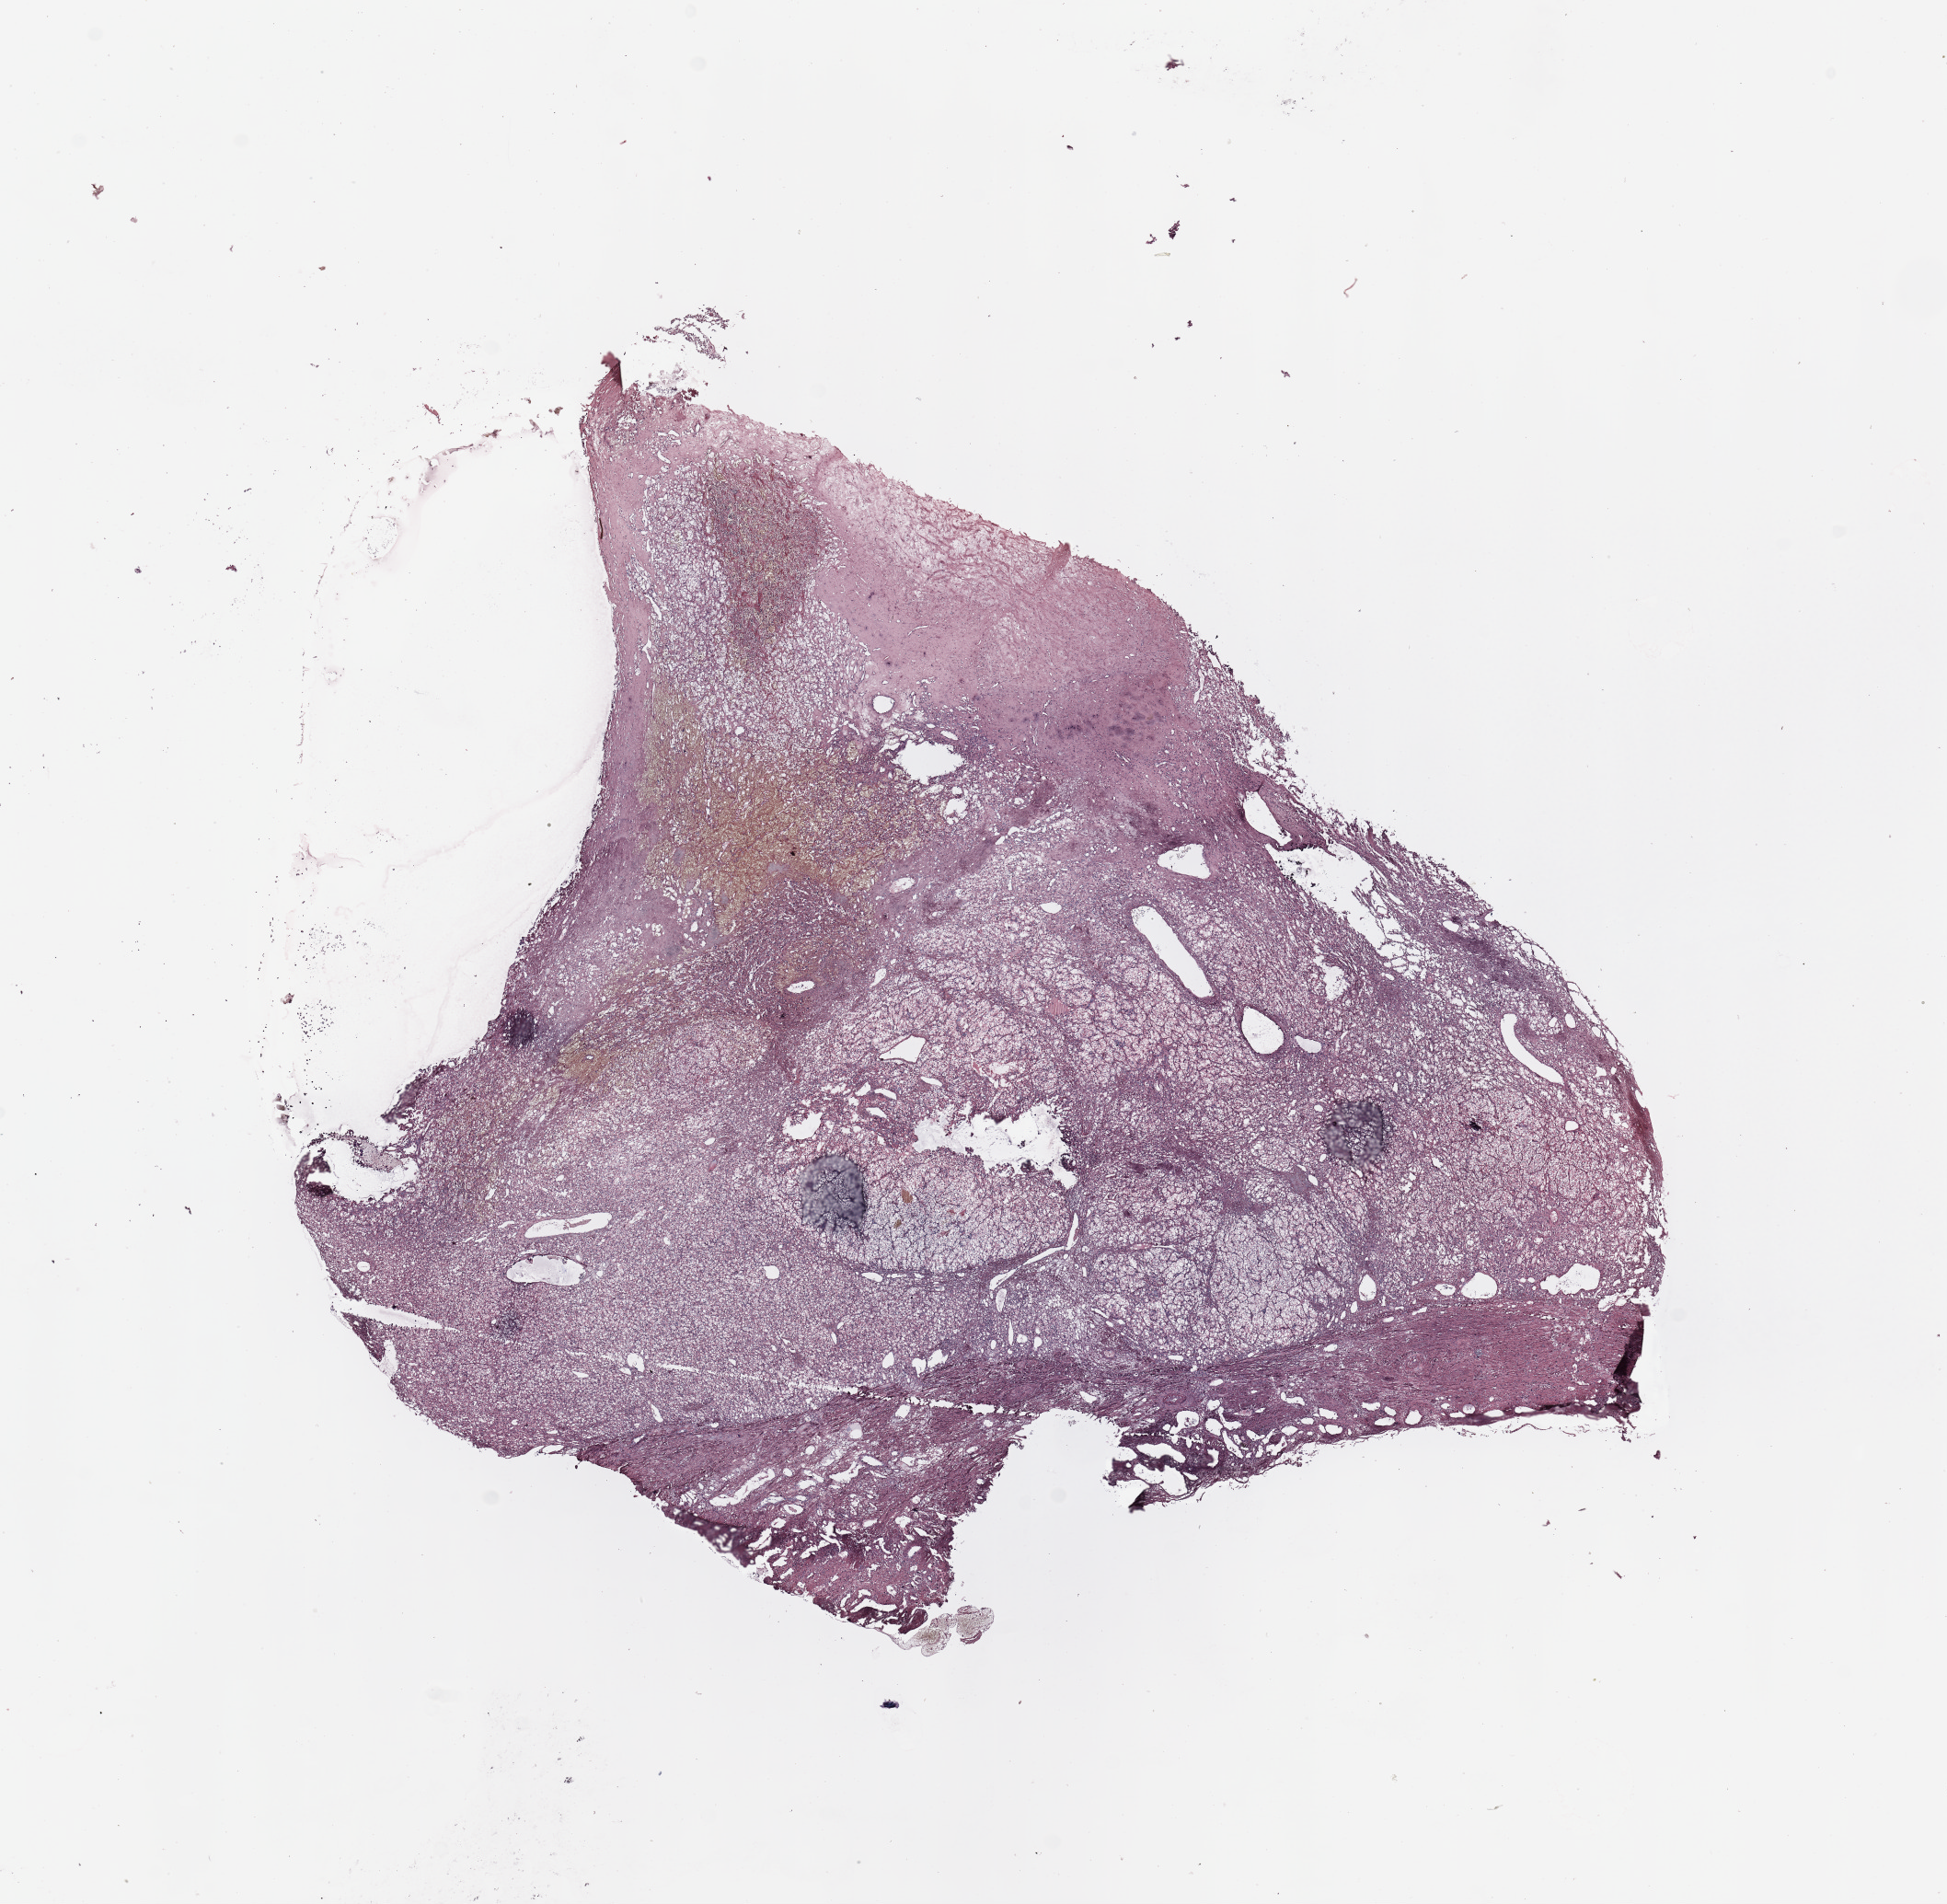
Digitized H&E tissue section (whole slide), shown as a low-resolution overview of the whole scanned area (about 16.7 x 16.4 mm, acquisition: 20x scan). Tumour tissue sample, sampled site: kidney. 56-year-old female patient. Histologic grade: G3 (poorly differentiated). Composition of this section per pathologist review: tumour nuclei 80%, necrosis 5%.
• histologic diagnosis: Renal cell carcinoma, NOS
• AJCC pathologic stage: IV